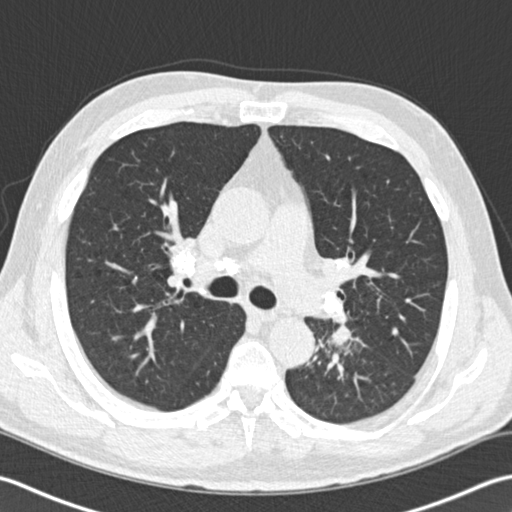
Low-dose screening chest CT, one axial slice. Position 110 of 170 along the scan axis. Reconstruction kernel B30f. 120 kVp. Lung window (W 1500 / L -600 HU). 512 × 512 image matrix, field of view 350 × 350 mm.
Outlined on this slice (outlined manually by an expert reader):
- lesion 1 (tumor, lower lobe of left lung): bounding box <331,325,352,345> (left, top, right, bottom; pixels)